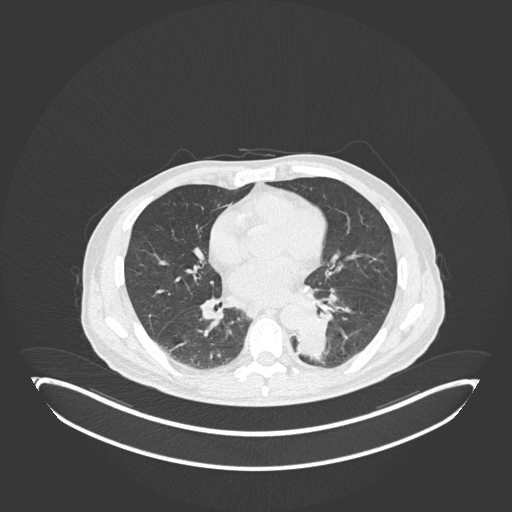
Chest CT, one axial slice. Position 83 of 251 along the scan axis. 120 kVp. Lung window (W 1500 / L -600 HU). 512 × 512 image matrix. Patient: male, 72 years. From the clinical record (not read from this slice): clinical TNM (as recorded): T2b N0 M1.
Structures marked on this image (bounding box drawn by a radiologist):
- lung tumour (recorded histology: adenocarcinoma): bounding box <296,319,333,364> (left, top, right, bottom; pixels)